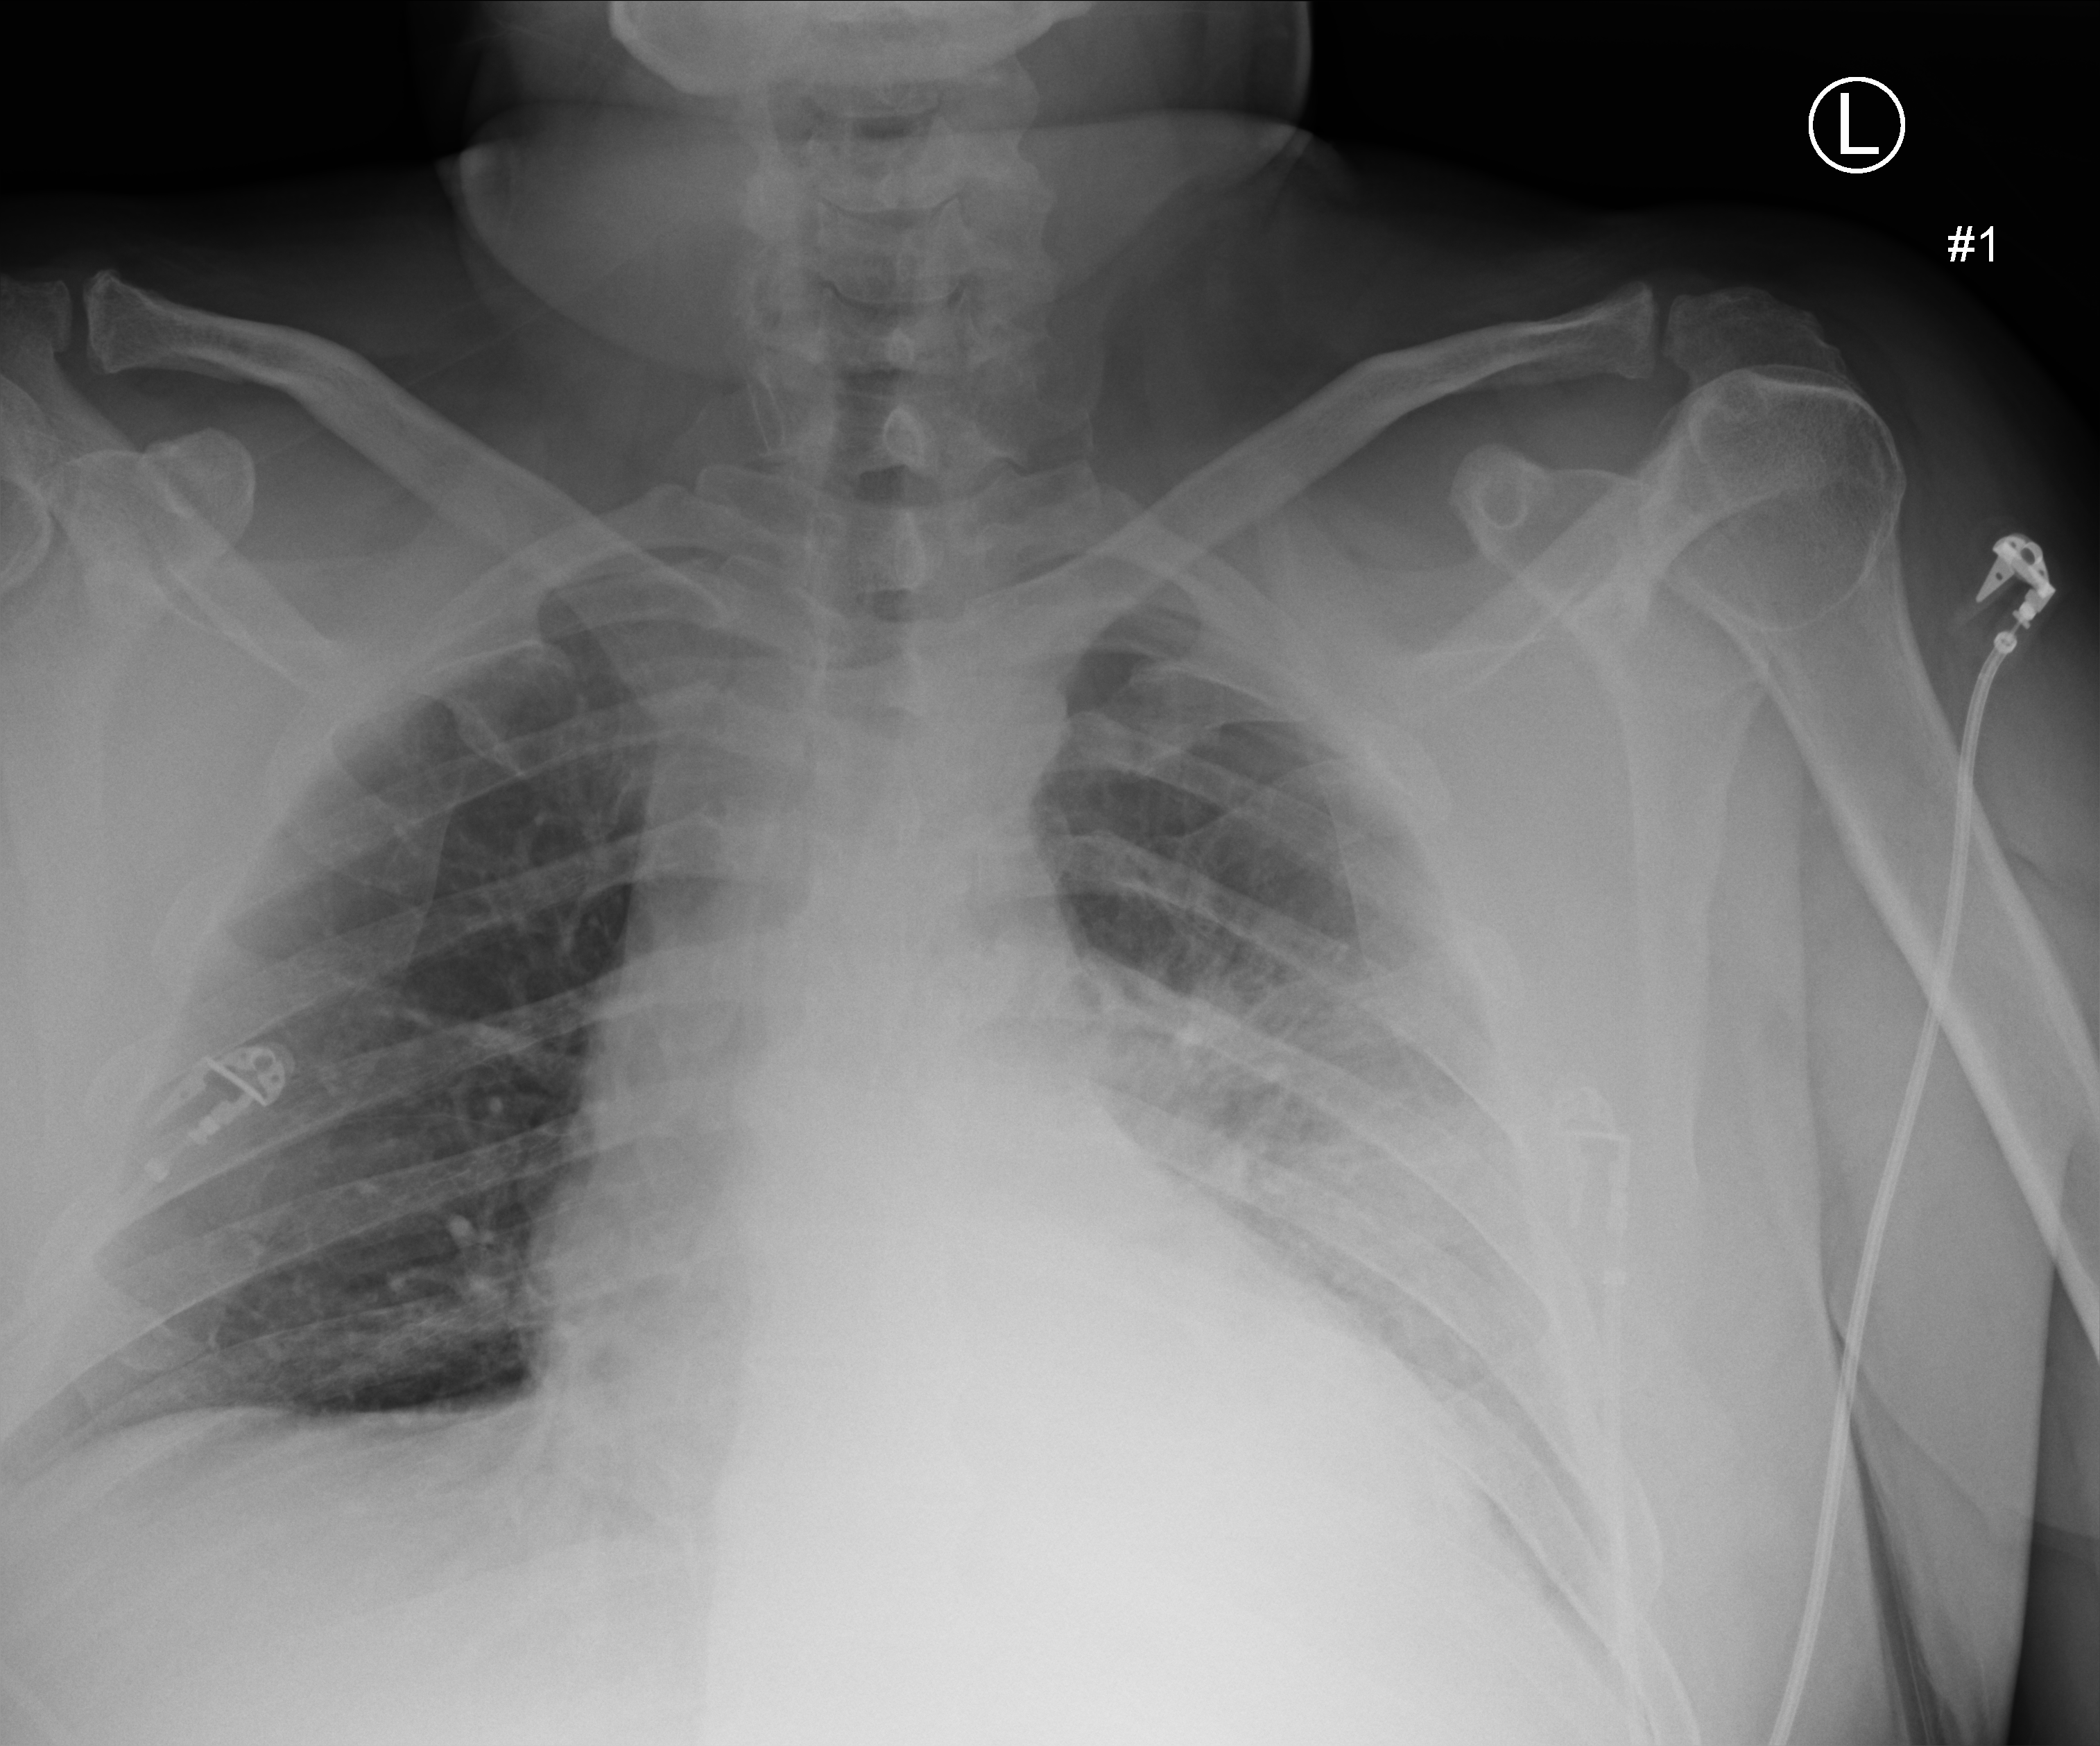
Portable chest radiograph; anteroposterior (AP) projection. Patient hospitalised with COVID-19; male, aged 18–59 years.
Admission-level facts for this patient (not findings on this image; timing relative to this image not recorded):
- admitted to intensive care during this hospital stay: no
- mechanically ventilated during this hospital stay: no